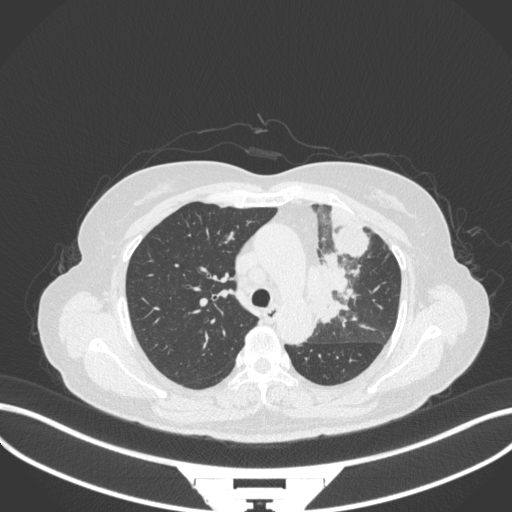
Chest CT, one axial slice. Position 233 of 382 along the scan axis. Lung window (W 1500 / L -600 HU). 1 mm slice thickness. 512 × 512 image matrix, field of view 400 × 400 mm. Female patient, age 64 years. Case-level facts recorded for this patient, not image findings: clinical TNM (as recorded): T2a N2 M0.
Annotated regions visible in this slice (rectangle marked by the reading radiologist):
- lung tumour (recorded histology: adenocarcinoma): bounding box (x1, y1, x2, y2) in pixels: (309, 251, 357, 327)
- lung tumour (recorded histology: adenocarcinoma): (332, 221, 375, 258)